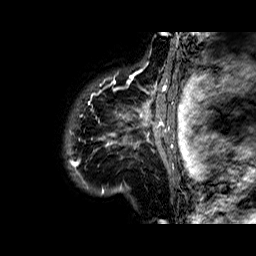
Breast MRI (dynamic contrast-enhanced), one sagittal slice. Position 59 of 60 along the scan axis. Dynamic contrast-enhanced series, time point 2 of 6 at this slice position (early post-contrast). 1.5 T. TE 6.3 ms, TR 32.4 ms. 4 mm slice thickness. 256 × 256 image matrix. Female patient. From the clinical record (not read from this slice): setting: breast cancer imaged before/during neoadjuvant chemotherapy; receptor status: HR-positive, HER2-negative.
Structures marked on this image (semi-automatically segmented with operator editing):
- analysis volume of interest (the breast-tissue region the enhancement analysis was run in; not a lesion): box from (x=68, y=72) to (x=177, y=183) px
- tumour enhancement mask (voxels above the 100 % enhancement threshold inside the analysis volume of interest): (x=70, y=72)–(x=173, y=167)